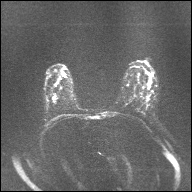
Breast MRI, one axial slice; slice 21 of 32 in the series (ordered by position); diffusion-weighted series; image 2 of 4 stored at this slice position (different b-values; order by instance number); 1.5 T; 4 mm slice thickness; 192 × 192 image matrix, field of view 360 × 360 mm. Female patient.
Outlined on this slice (manually delineated by an expert):
- tumour on diffusion-weighted imaging: box from (x=53, y=96) to (x=56, y=100) px